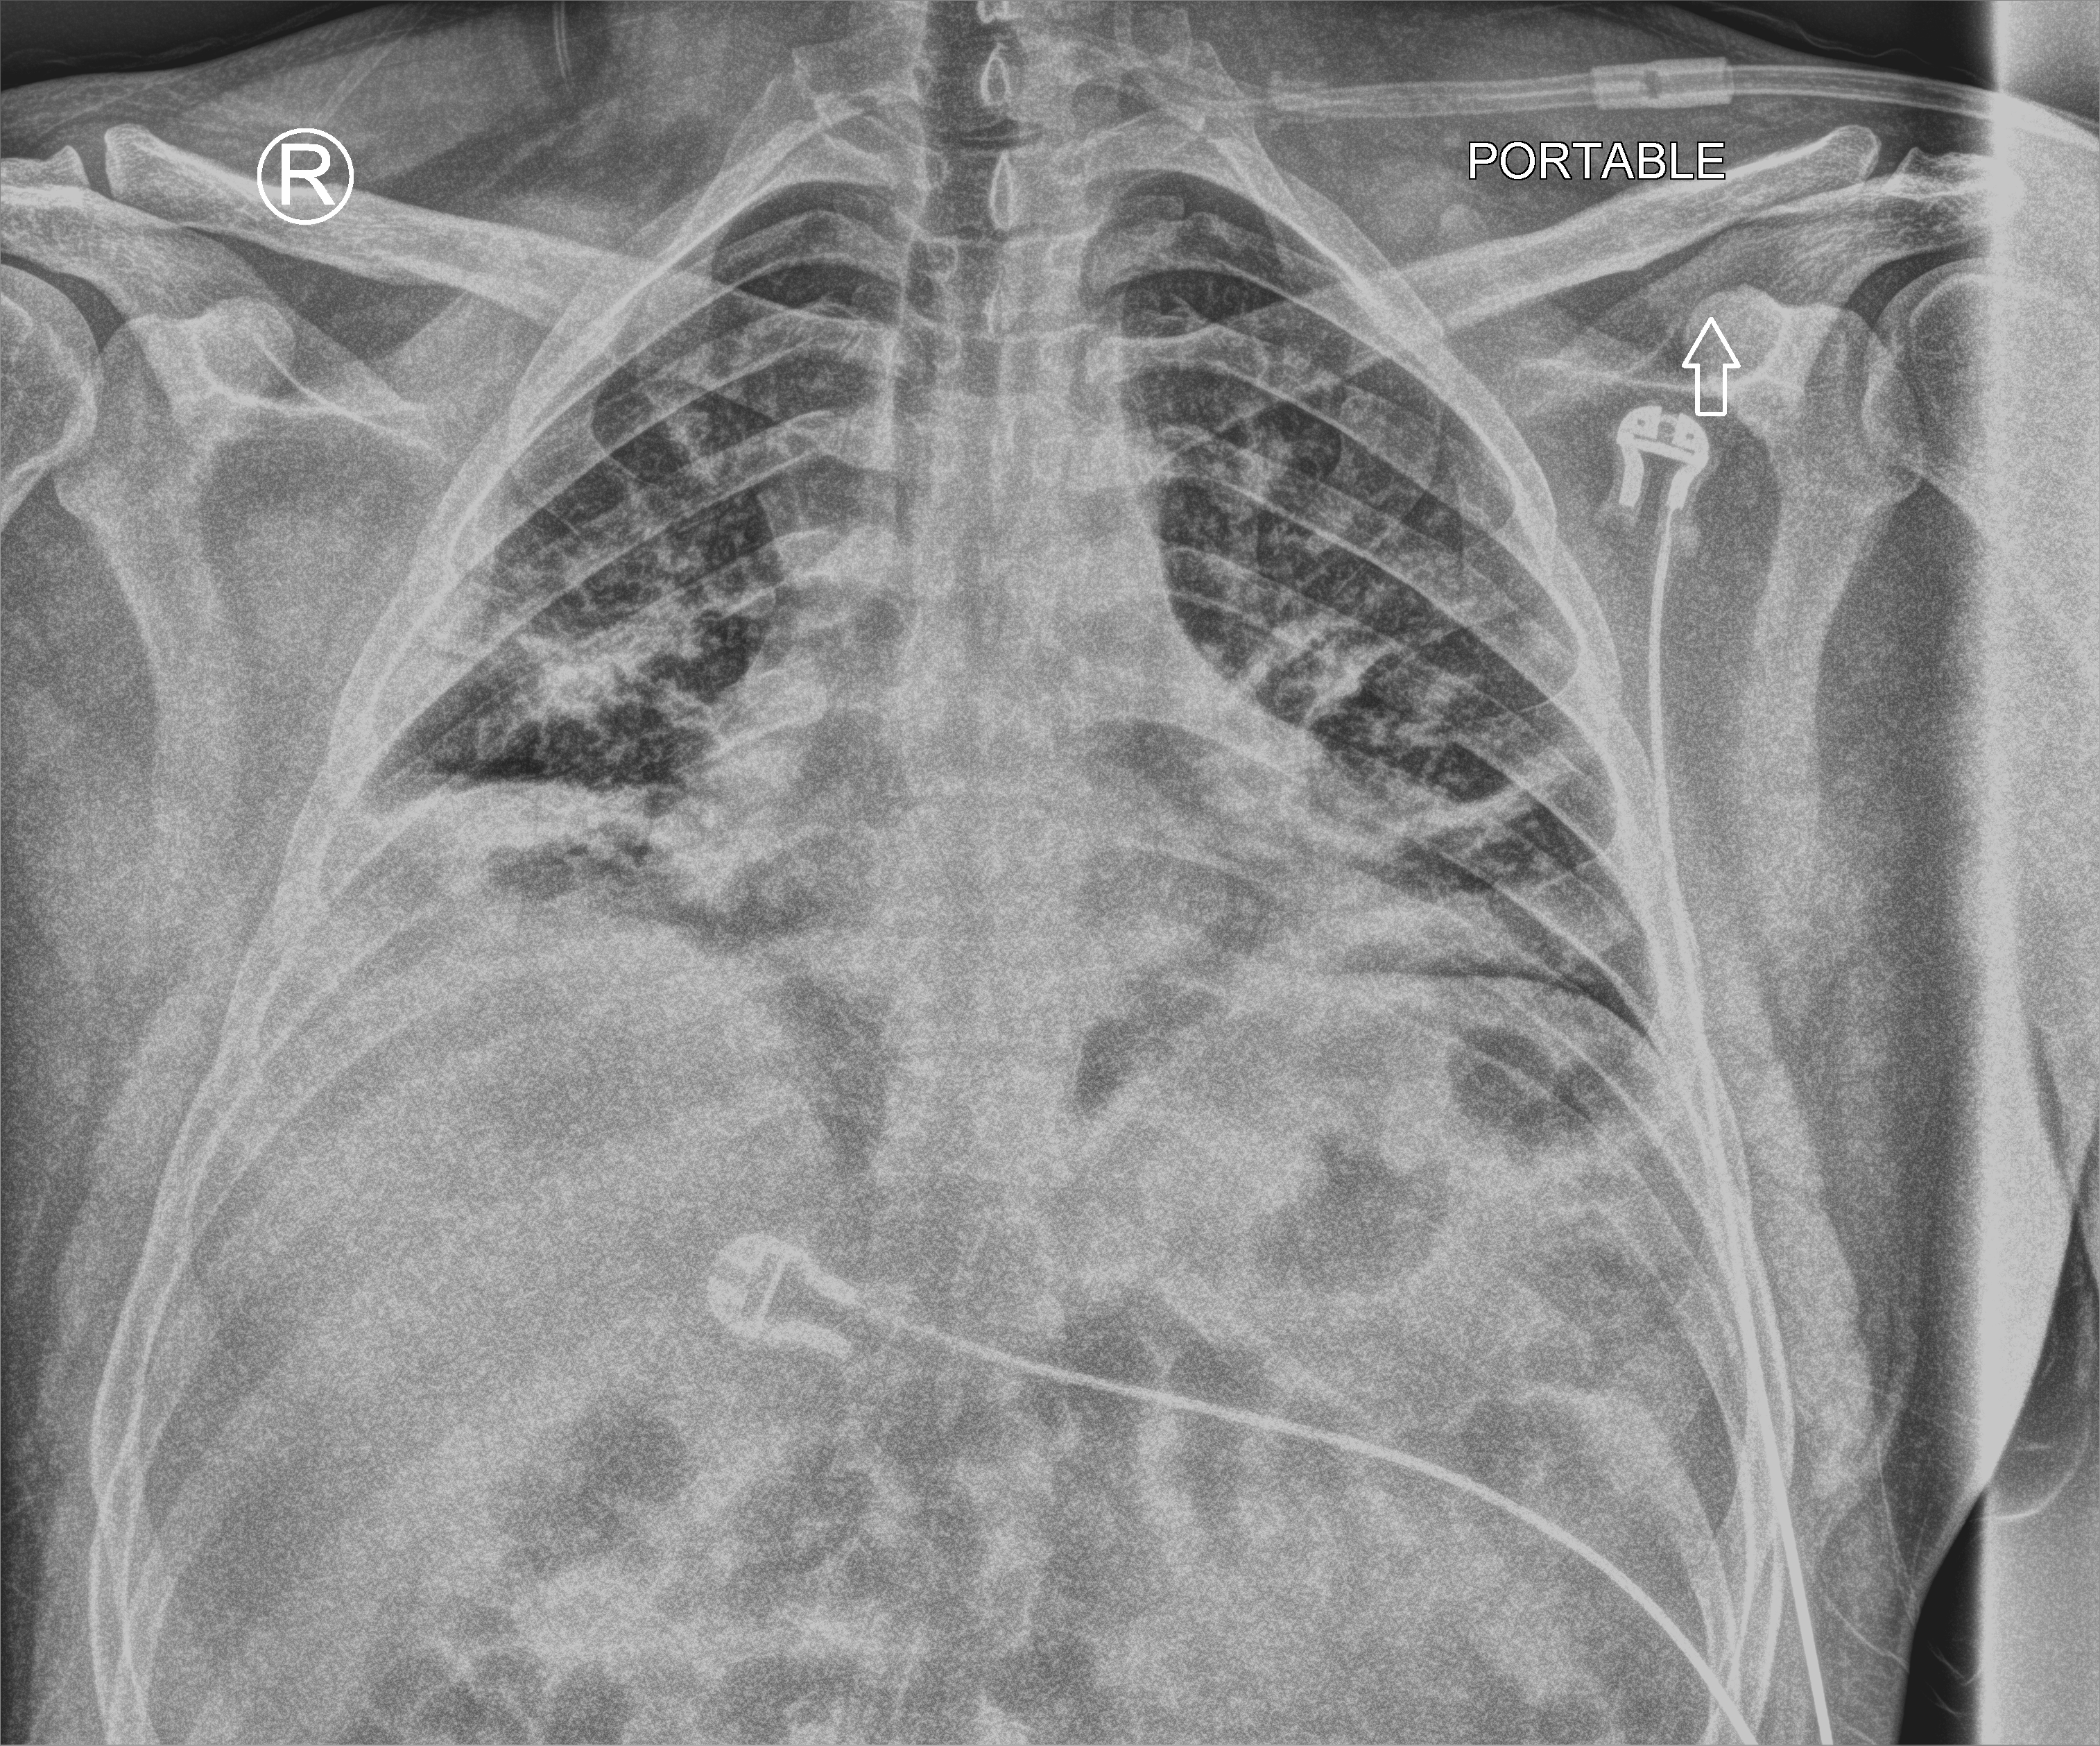
Chest X-ray (portable); anteroposterior (AP) projection. Patient hospitalised with COVID-19; male, aged 18–59 years.
From the hospital-stay record, not from the radiograph (when in the stay this image was taken is not recorded): mechanically ventilated during this hospital stay: no.